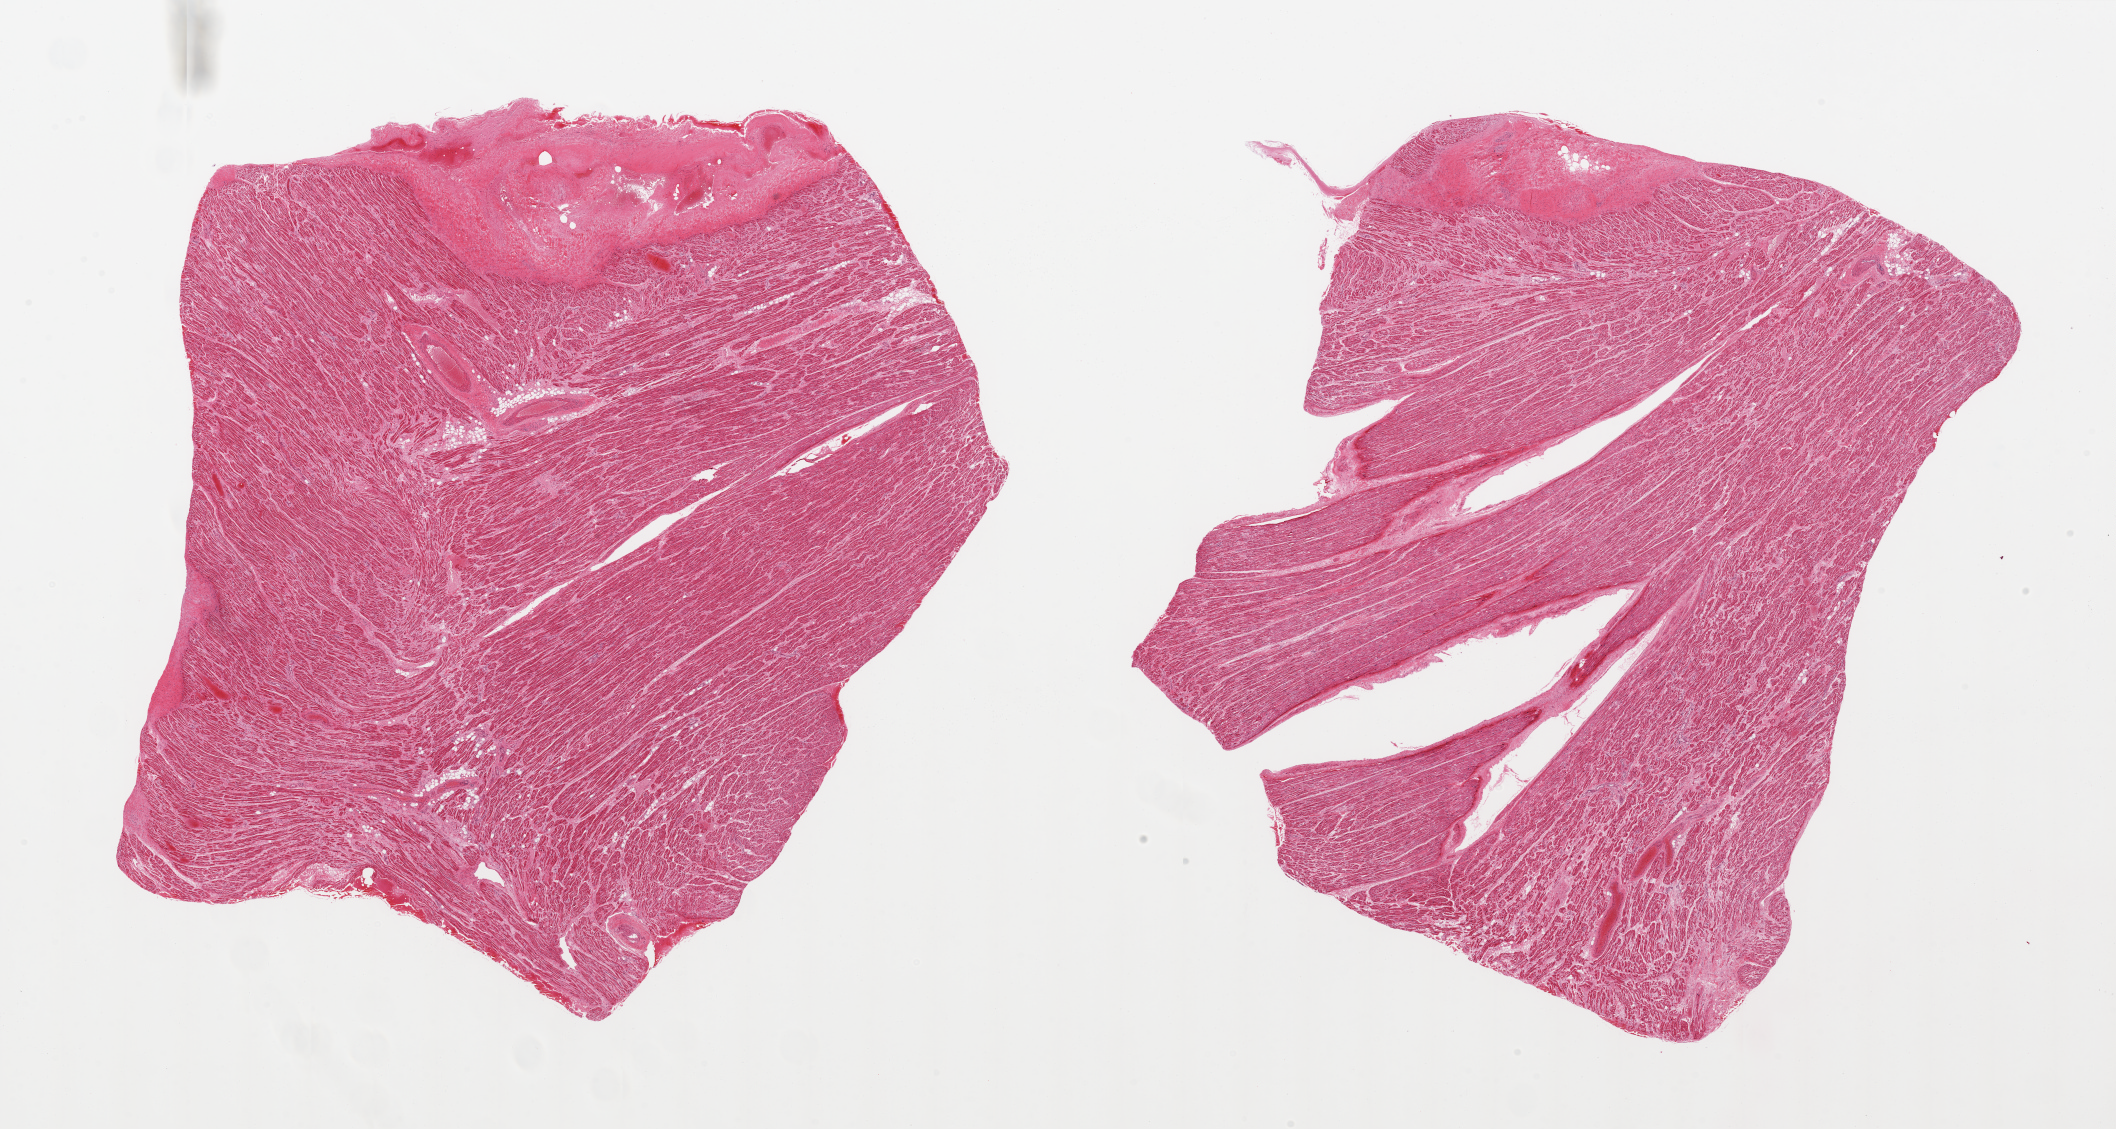
Hematoxylin and eosin (H&E) whole-slide image, brightfield, low-resolution overview of the scanned area, about 33.5 x 17.9 mm (slide scanned at 20x); PAXgene-fixed, paraffin-embedded tissue; section of auricular appendage (target tissue); tissue donor sample. Male donor.
Review note (as recorded): 2 pieces, myocardial infarction, diffuse interstitial fibrosis.